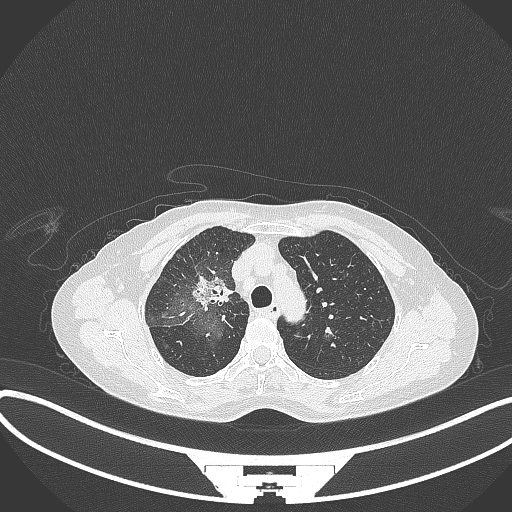
Chest CT, one axial slice; position 238 of 284 along the scan axis; reconstruction kernel B70f; lung window (W 1500 / L -600 HU); 1 mm slice thickness; 512 × 512 image matrix, field of view 400 × 400 mm. Patient: female, 59 years. From the clinical record (not read from this slice): clinical TNM (as recorded): T3 N0 M0; histopathological grade: G1.
Outlined on this slice (bounding box drawn by a radiologist):
- lung tumour (recorded histology: adenocarcinoma): box from (x=190, y=268) to (x=234, y=309) px